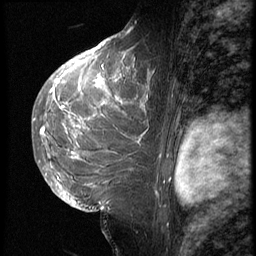
Breast MRI (dynamic contrast-enhanced), one sagittal slice. Position 37 of 62 along the scan axis. 3 images stored at this slice position (order not interpretable as contrast timing). 1.5 T. TE 4.2 ms, TR 9 ms. 2.5 mm slice thickness. 256 × 256 image matrix, field of view 180 × 180 mm. Female patient, age 28 years. Case-level facts recorded for this patient, not image findings: setting: breast cancer imaged before/during neoadjuvant chemotherapy.
Outlined on this slice (semi-automatic segmentation, software-assisted and operator-edited):
- analysis volume of interest (the breast-tissue region the enhancement analysis was run in; not a lesion): bounding box (x1, y1, x2, y2) in pixels: (42, 45, 161, 207)
- tumour enhancement mask (voxels above the 140 % enhancement threshold inside the analysis volume of interest): (42, 45, 147, 157)